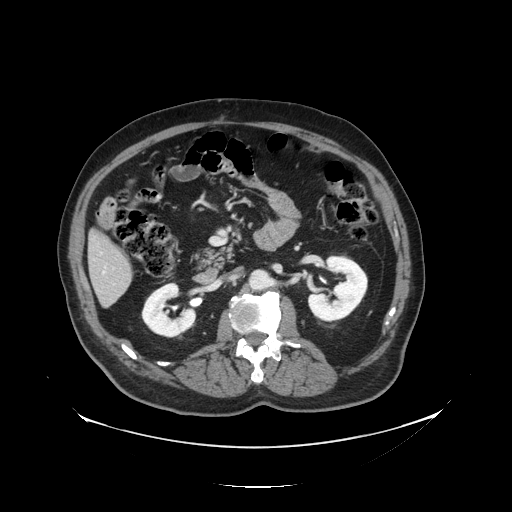
Contrast-enhanced abdominal CT, one axial slice; slice 49 of 138 in the series (ordered by position); 120 kVp; soft-tissue window (W 400 / L 40 HU); 2.5 mm slice thickness; 512 × 512 image matrix. Male patient, age 77 years. From the clinical record (not read from this slice): diagnosis: colorectal cancer liver metastases, imaged before liver resection; multiple liver metastases: no; largest metastasis: 1.5 cm; disease in both lobes: no.
Annotated regions visible in this slice (outlined manually by an expert reader):
- liver: box from (x=90, y=236) to (x=134, y=307) px
- planned liver remnant (the part of the liver to remain after resection): (x=90, y=236)–(x=131, y=279)